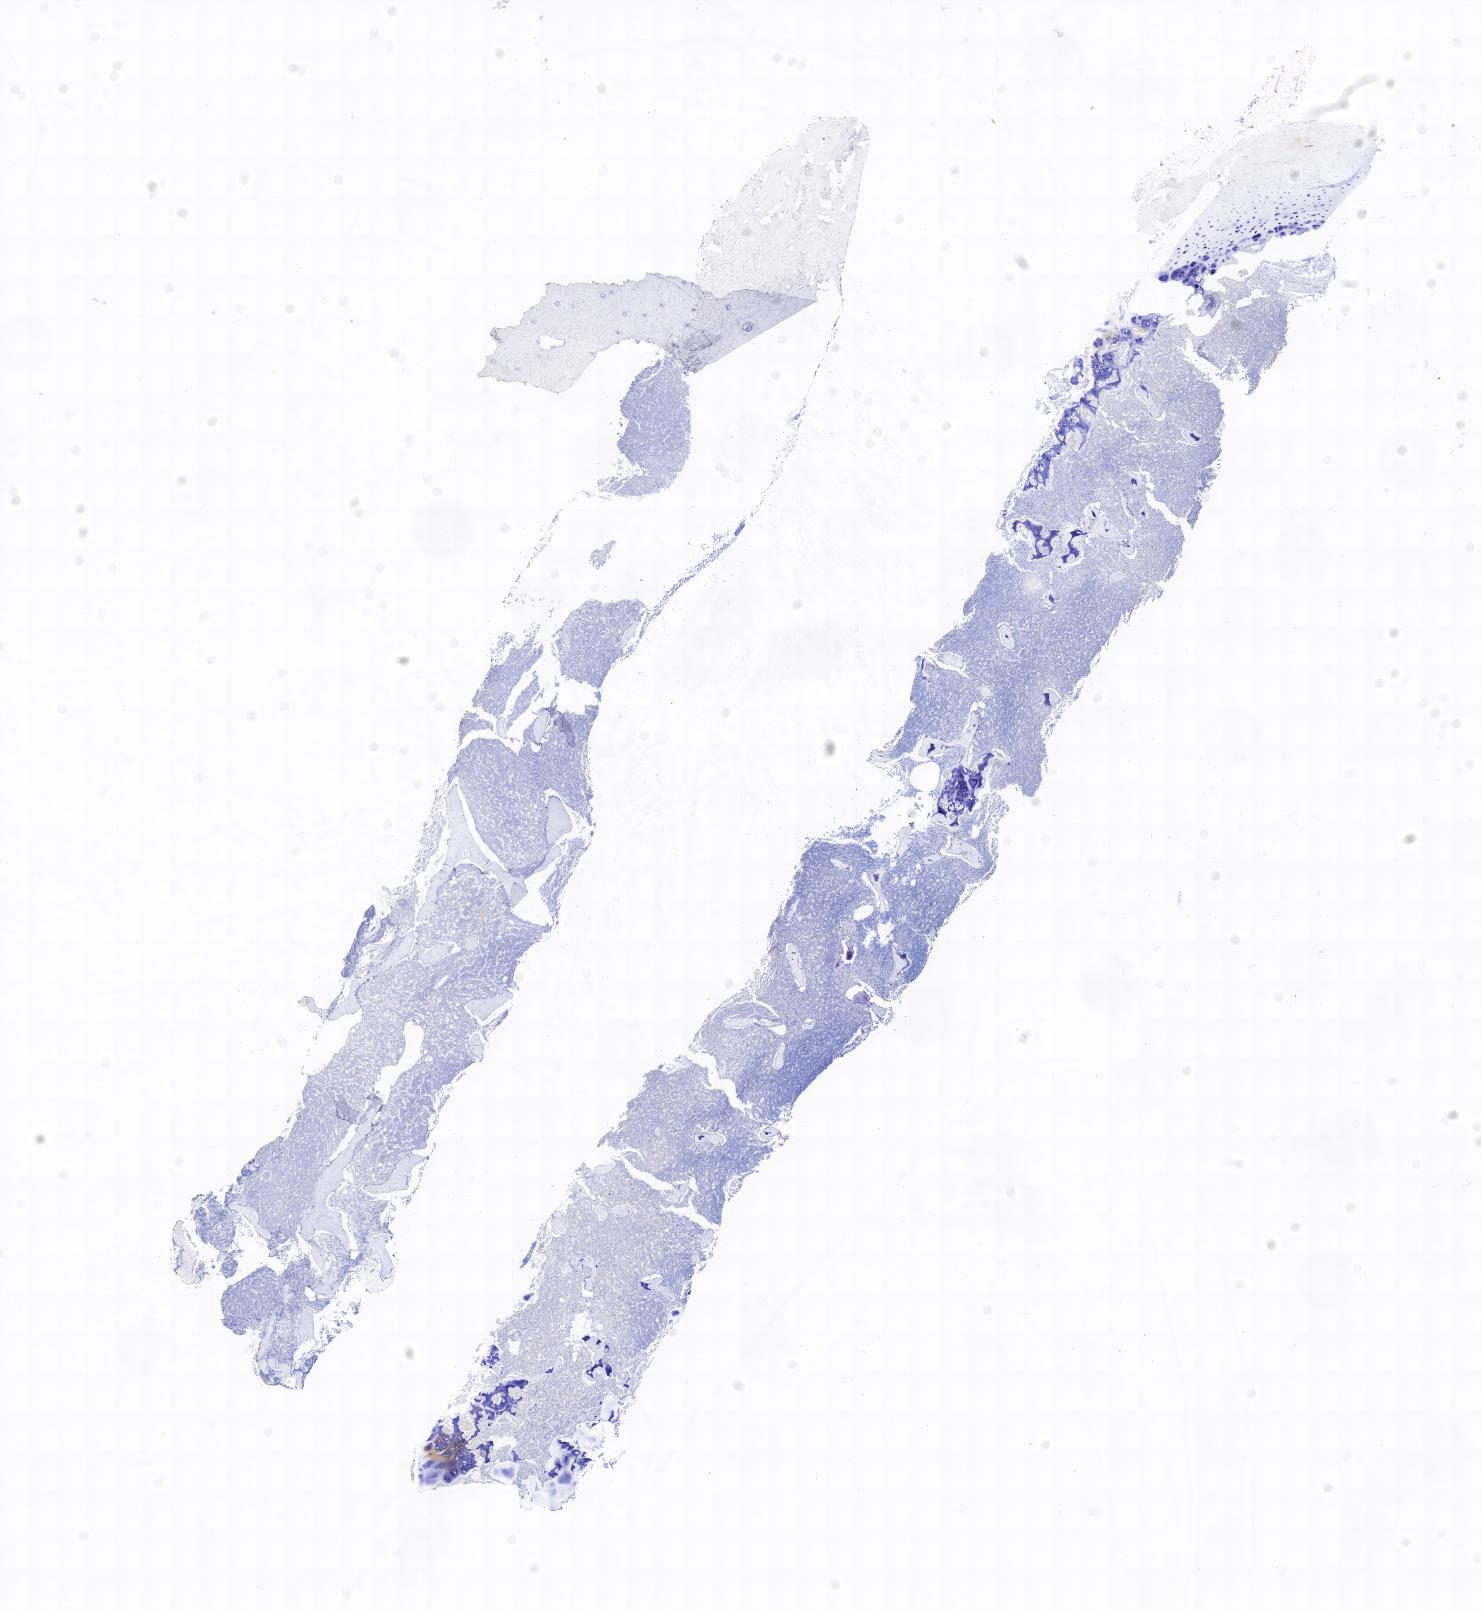
Immunohistochemistry (IHC) whole-slide image stained for BCL2, a low-resolution overview of the entire scanned area. Specimen: tumor tissue. Anatomic site: bone marrow. Patient: male, 16 years old.
Diagnosis: Burkitt lymphoma, NOS.